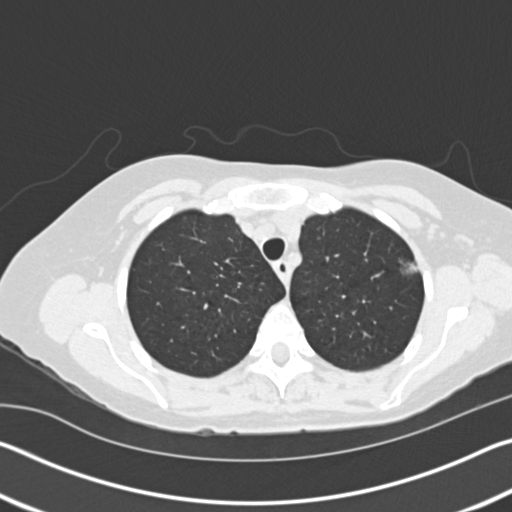
Chest CT (low-dose screening protocol), one axial image; baseline annual screen; lung window (W 1500 / L -600 HU); 2 mm slice thickness; 120 kVp; slice 33 of 154 in the series; 512 × 512 image matrix. Female, age 60 years at enrolment. Former smoker at enrolment.
- Lesion marked by an expert reader, box from (x=384, y=245) to (x=436, y=287) px.
- The screening reader recorded 2 non-calcified nodules or masses ≥4 mm on this exam (right lower lobe, left upper lobe); which of them this box marks is not recorded.
- Official screen result: positive, change unspecified: nodule(s) >= 4 mm or enlarging nodule(s), mass(es), or other non-specific abnormalities suspicious for lung cancer.